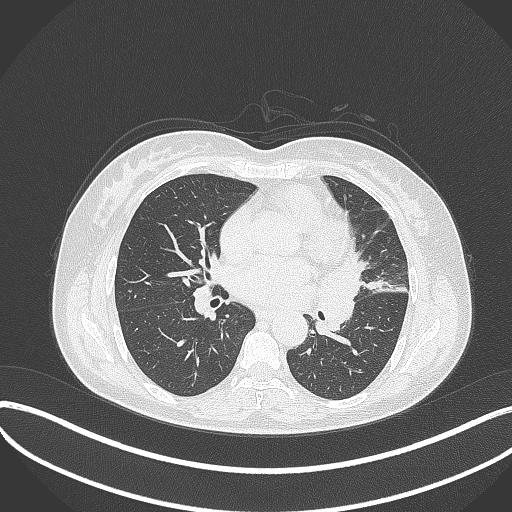
Chest CT, one axial slice. Slice 175 of 373 in the series (ordered by position). Reconstruction kernel B70f. 120 kVp. Lung window (W 1500 / L -600 HU). 1 mm slice thickness. 512 × 512 image matrix, field of view 400 × 400 mm. Female patient, age 54 years. Case-level facts recorded for this patient, not image findings: clinical TNM (as recorded): T2a N1 M0; histopathological grade: G3.
Annotated regions visible in this slice (rectangle marked by the reading radiologist):
- lung tumour (recorded histology: small cell carcinoma): bounding box <319,255,368,342> (left, top, right, bottom; pixels)